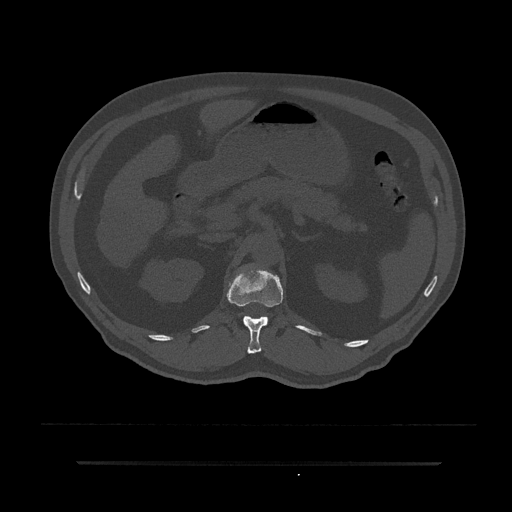
CT including the spine, one axial slice. Slice 190 of 797 in the series (ordered by position). Reconstruction kernel Br40s/3. 120 kVp. Bone window (W 1800 / L 400 HU). 0.5 mm slice thickness. 512 × 512 image matrix, field of view 464 × 464 mm. Male patient, age 59 years. From the clinical record (not read from this slice): primary cancer: bile ducts; vertebrae with lytic lesions (as recorded): T10.
Structures marked on this image (semi-automatic segmentation, software-assisted and operator-edited):
- T12 vertebra: bounding box [x1, y1, x2, y2] px = [226, 267, 283, 354]